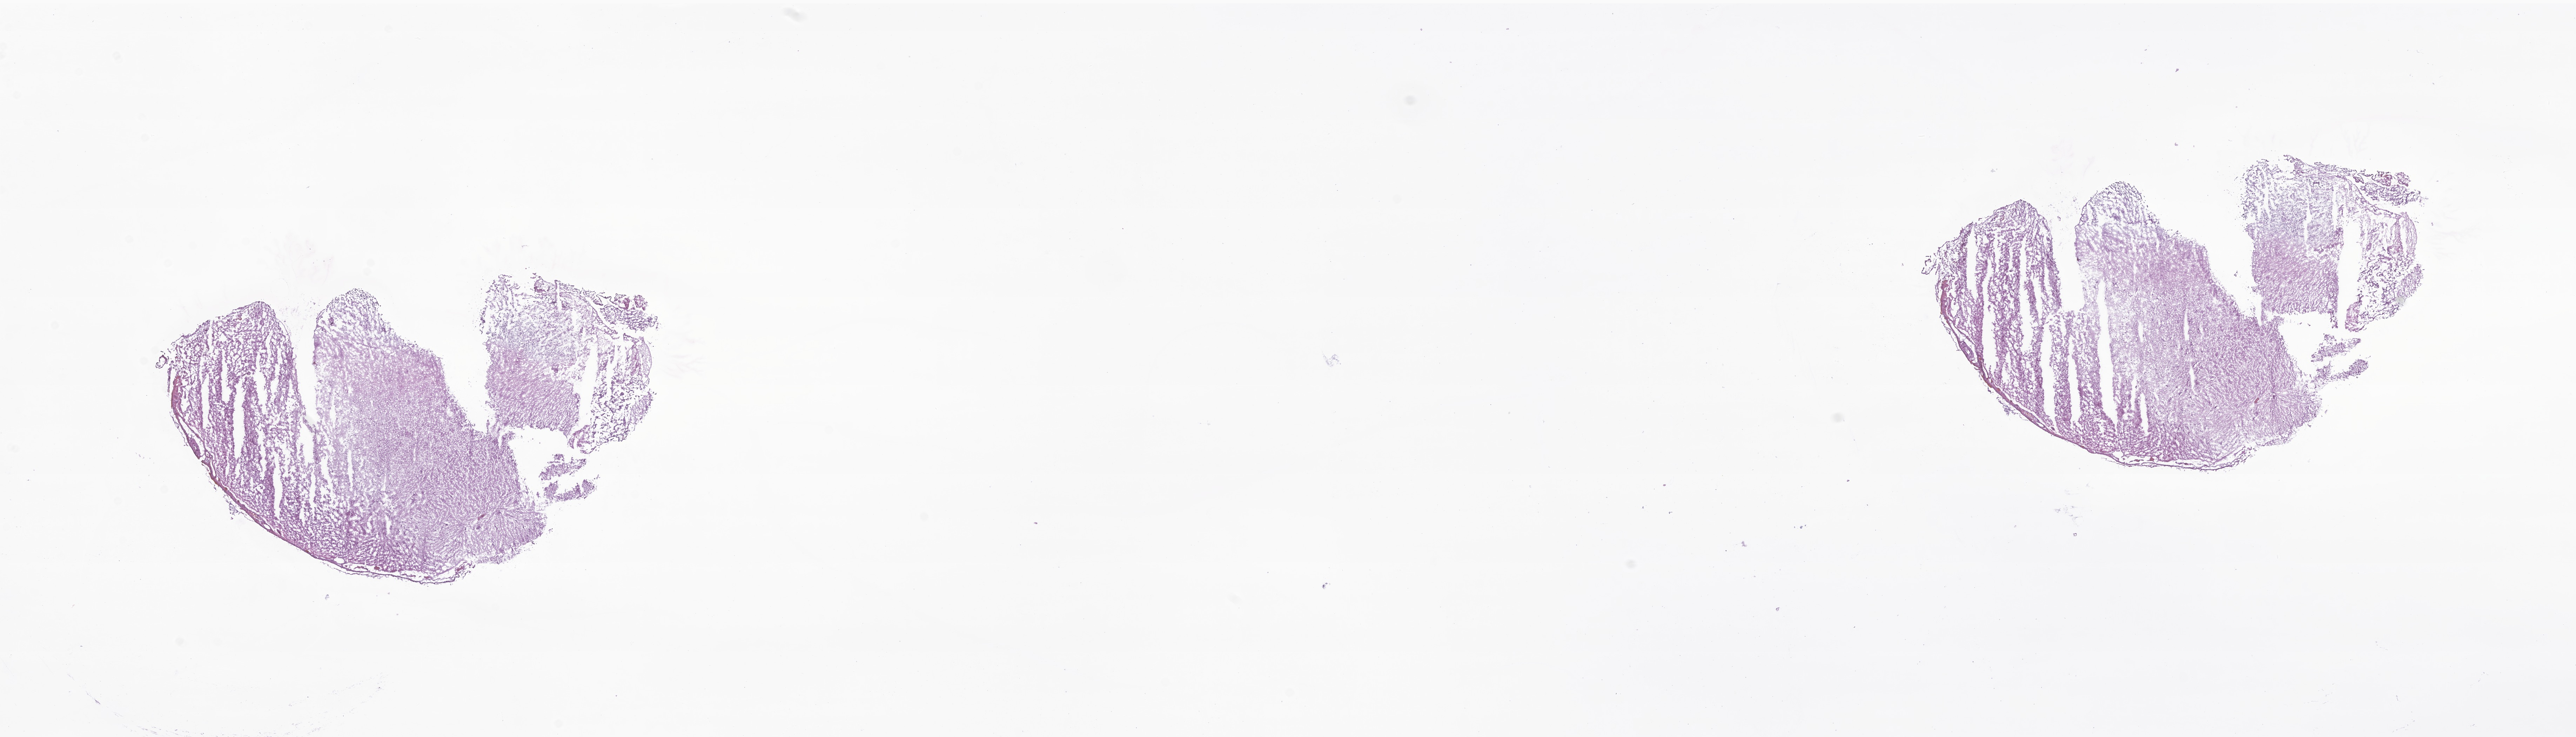
Haematoxylin and eosin whole-slide image of tumor tissue from the brain — low-resolution overview of the scanned area, about 31.0 x 8.9 mm. Frozen section (OCT-embedded). Patient female; age 997 days (about 2.7 years).
Diagnosis (ICD-O-3 morphology term): Ewing sarcoma.